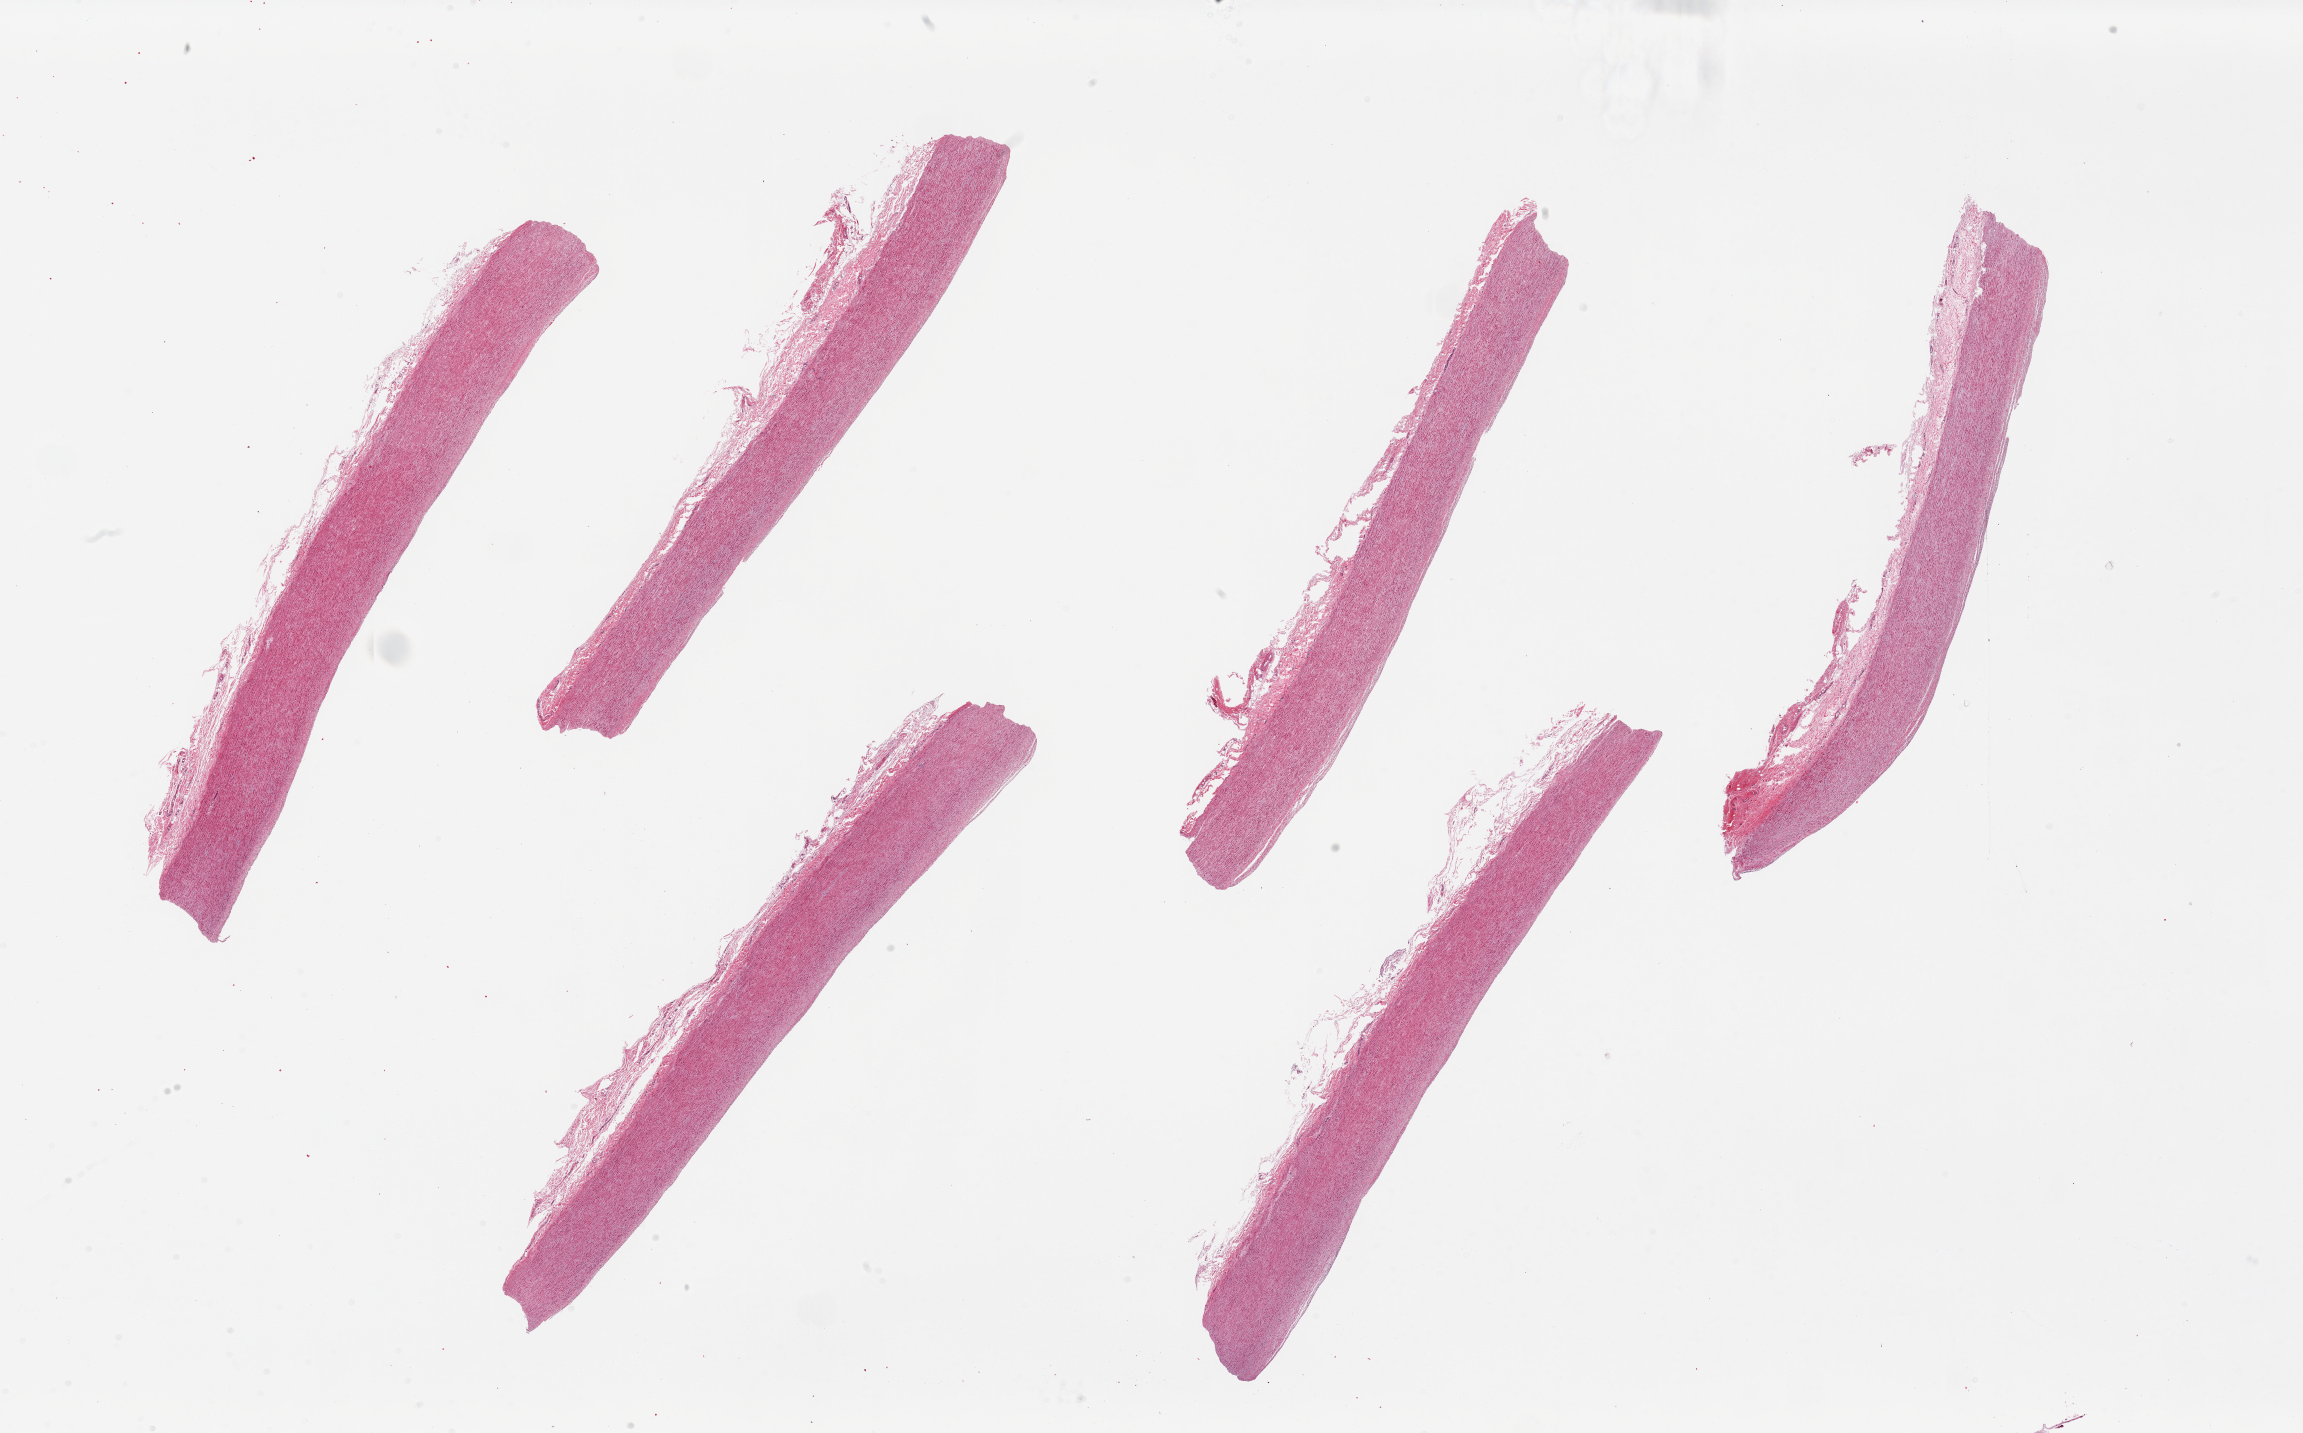
Digitized H&E-stained section, brightfield, whole scanned area (about 36.4 x 22.7 mm) shown as a low-resolution overview; PAXgene-fixed, paraffin-embedded tissue; section of aorta (target tissue); donor tissue sample. Donor sex: female.
• pathologist's review note for this sample: 6 pieces. up to 12.5x2.5mm; Adventitial extraneous stroma is up to 0.6 mm. No plaques